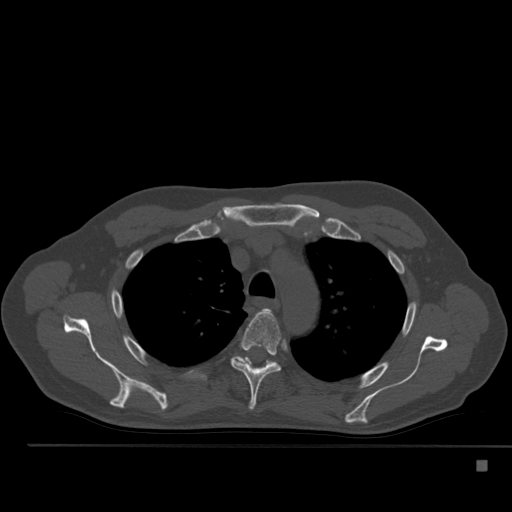
CT including the spine, one axial slice. Position 380 of 517 along the scan axis. Reconstruction kernel Br40s. Bone window (W 1800 / L 400 HU). 1.5 mm slice thickness. 512 × 512 image matrix. Patient: male, 70 years. From the clinical record (not read from this slice): primary cancer: renal; vertebrae with lytic lesions (as recorded): T4, T6, T10, T12, L3, L4, L5.
Structures marked on this image (semi-automatically segmented with operator editing):
- T3 vertebra: bounding box (x1, y1, x2, y2) in pixels: (265, 309, 271, 311)
- T4 vertebra: (230, 309, 282, 410)
- T5 vertebra: (236, 357, 273, 365)